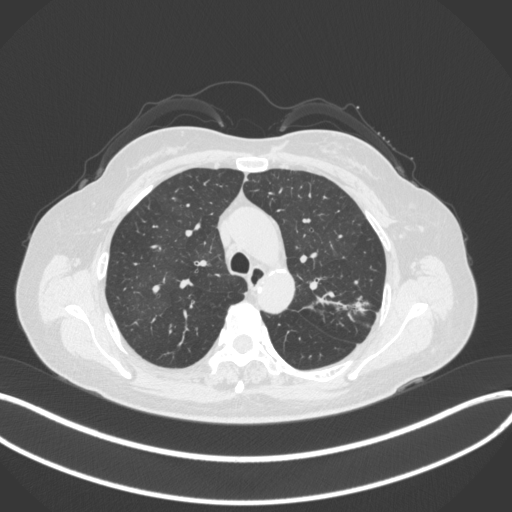
Chest CT, one axial slice. Position 246 of 330 along the scan axis. Reconstruction kernel B31f. 120 kVp. Lung window (W 1500 / L -600 HU). 1 mm slice thickness. 512 × 512 image matrix, field of view 400 × 400 mm. Female patient, age 60 years. Case-level facts recorded for this patient, not image findings: clinical TNM (as recorded): T1c N0 M0.
Annotated regions visible in this slice (rectangle marked by the reading radiologist):
- lung tumour (recorded histology: adenocarcinoma): bounding box [x1, y1, x2, y2] px = [344, 295, 370, 320]